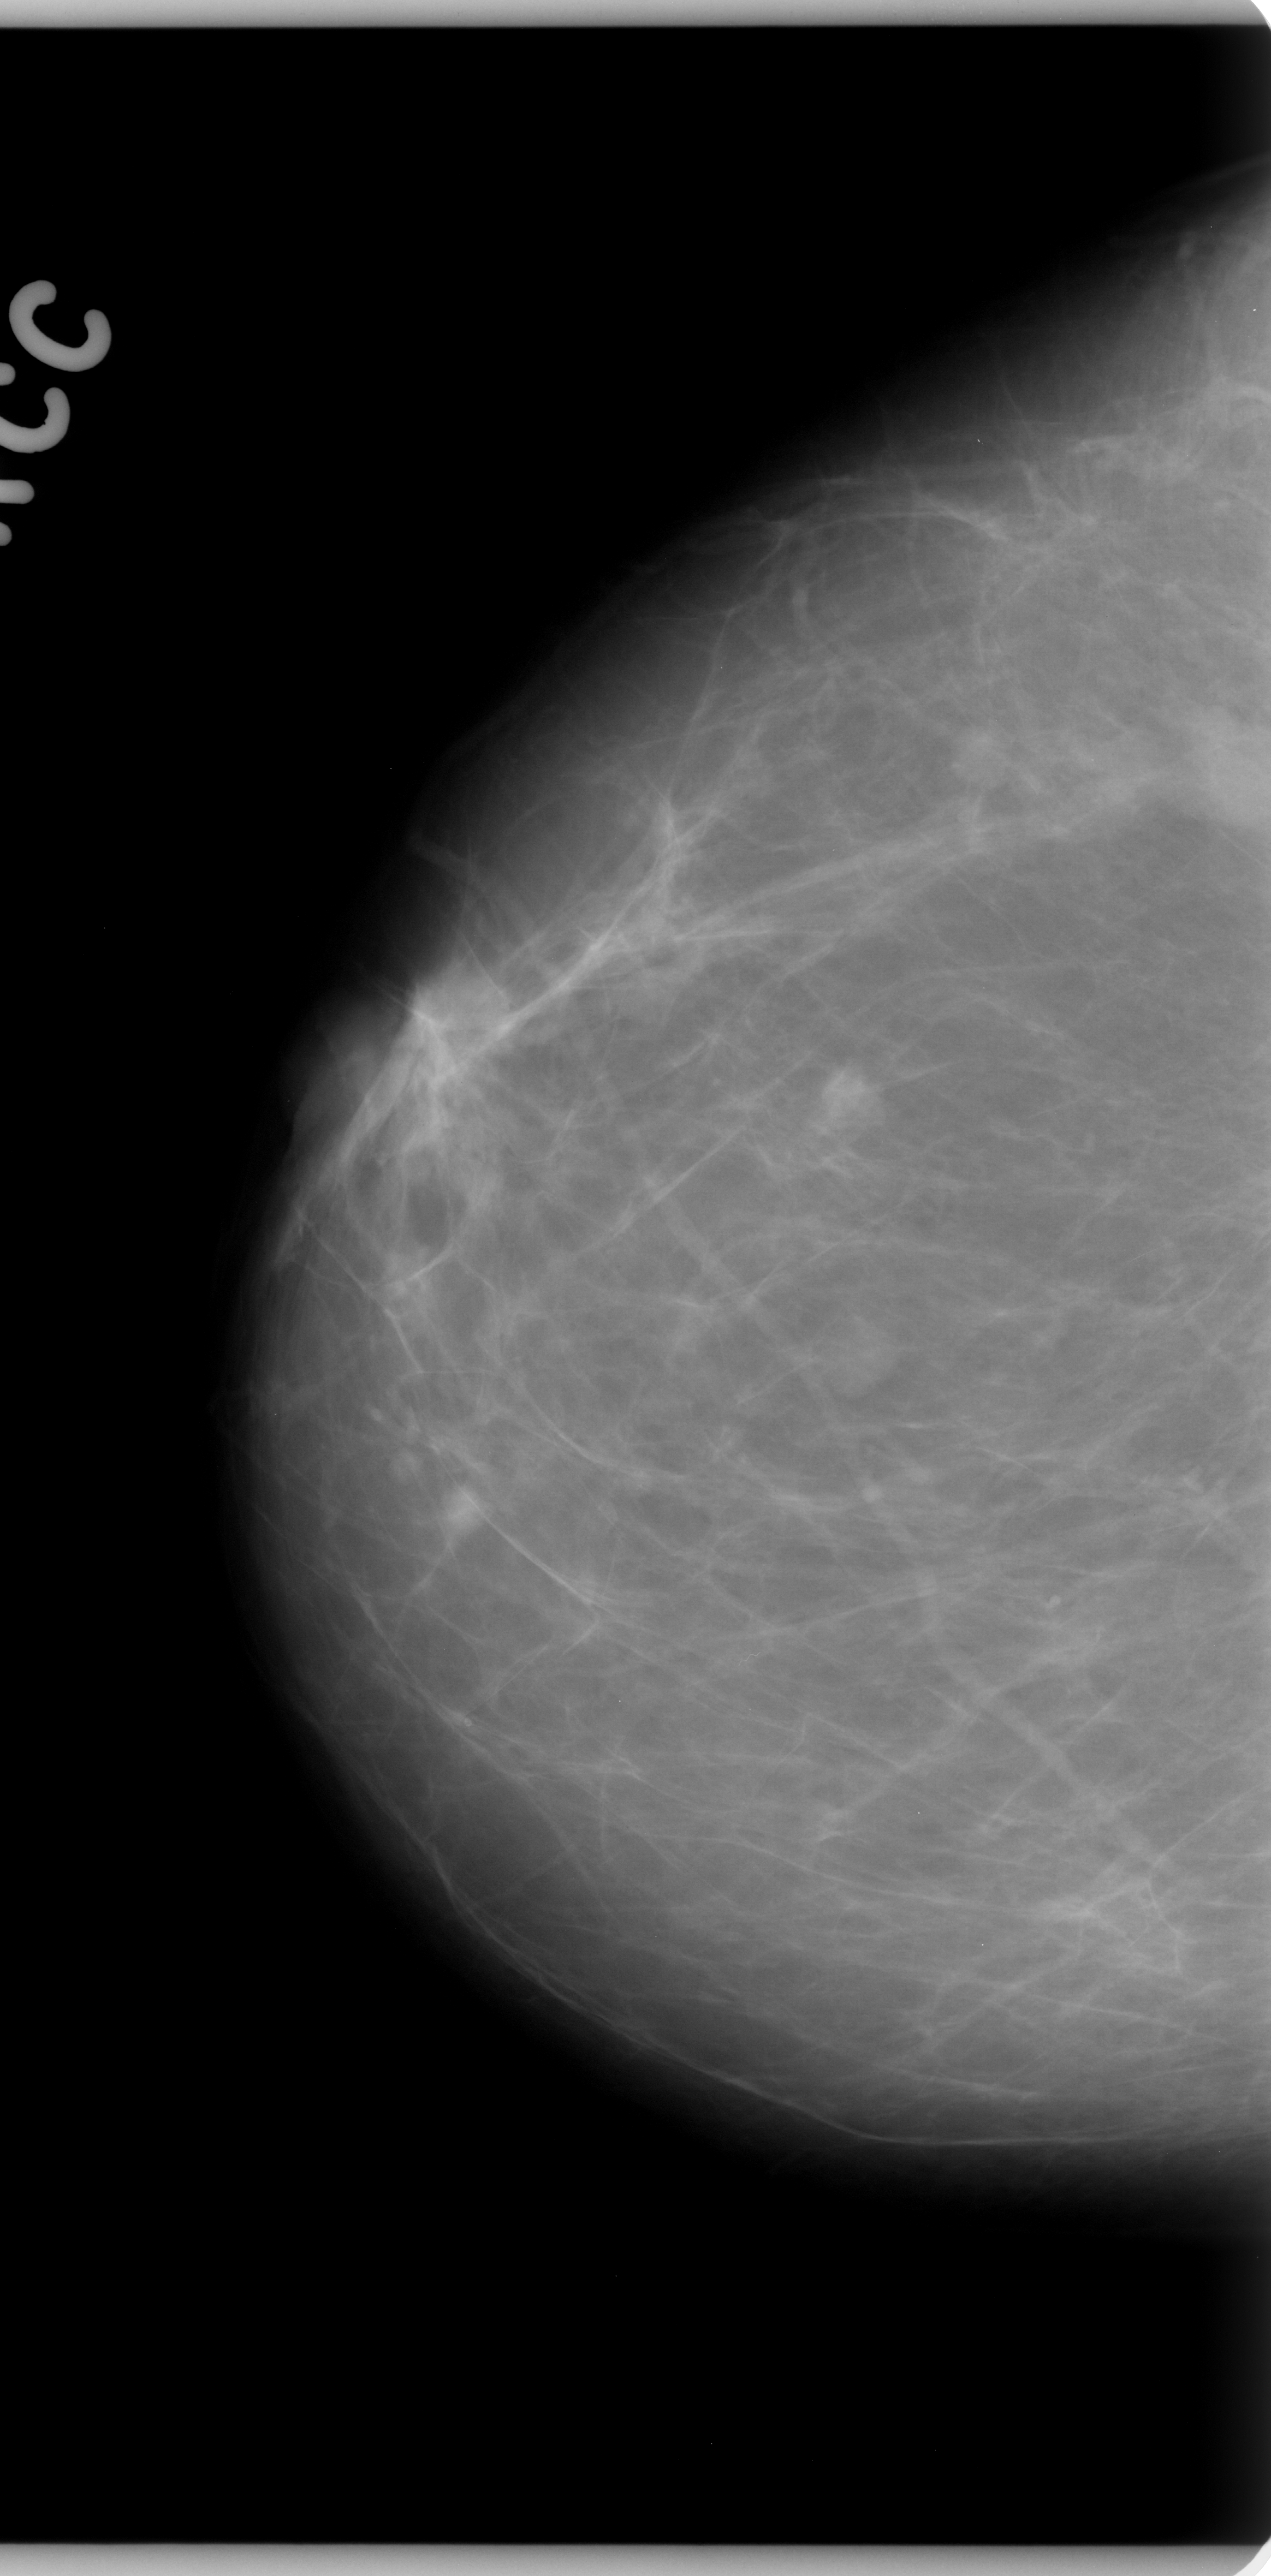
Digitized screen-film mammogram. Right breast. Craniocaudal (CC) view. Breast composition: almost entirely fatty (BI-RADS density category 1 of 4). 1271 × 2576 image matrix.
Expert-marked regions of interest on this image (one box per marked abnormality):
- mass, shape oval, margins spiculated; BI-RADS assessment category 5; pathology result (as recorded, not read from the image): malignant: box from (x=378, y=976) to (x=539, y=1152) px